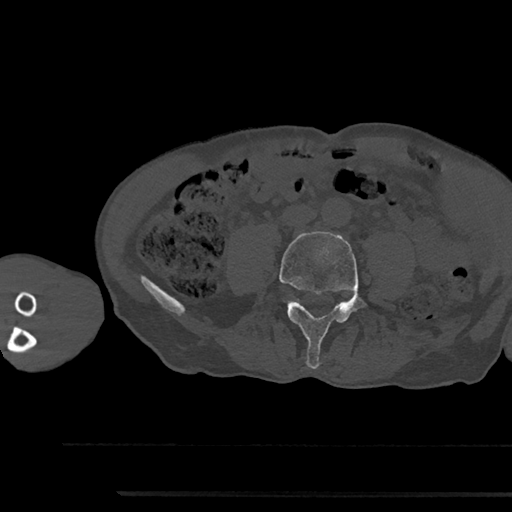
CT including the spine, one axial slice. Slice 406 of 797 in the series (ordered by position). Bone window (W 1800 / L 400 HU). 0.5 mm slice thickness. 512 × 512 image matrix, field of view 367 × 367 mm. Male patient, age 79 years. From the clinical record (not read from this slice): primary cancer: prostate.
Structures marked on this image (semi-automatically segmented with operator editing):
- L4 vertebra: bounding box <279,231,362,369> (left, top, right, bottom; pixels)